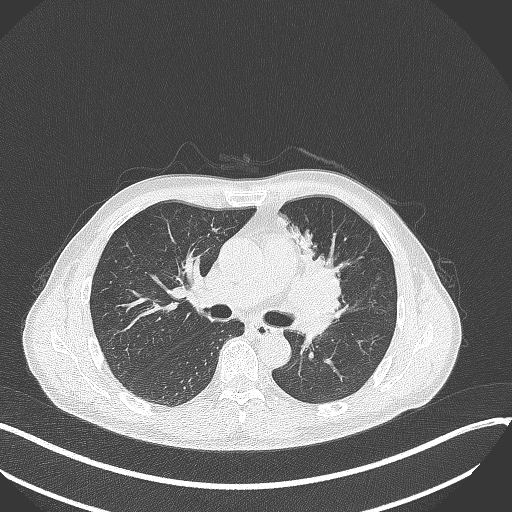
Chest CT, one axial slice; position 199 of 411 along the scan axis; reconstruction kernel B70f; lung window (W 1500 / L -600 HU); 1 mm slice thickness; 512 × 512 image matrix, field of view 400 × 400 mm. Male patient, age 56 years. From the clinical record (not read from this slice): clinical TNM (as recorded): T2a N0 M0.
Outlined on this slice (rectangle marked by the reading radiologist):
- lung tumour (recorded histology: squamous cell carcinoma): bounding box <287,231,351,322> (left, top, right, bottom; pixels)